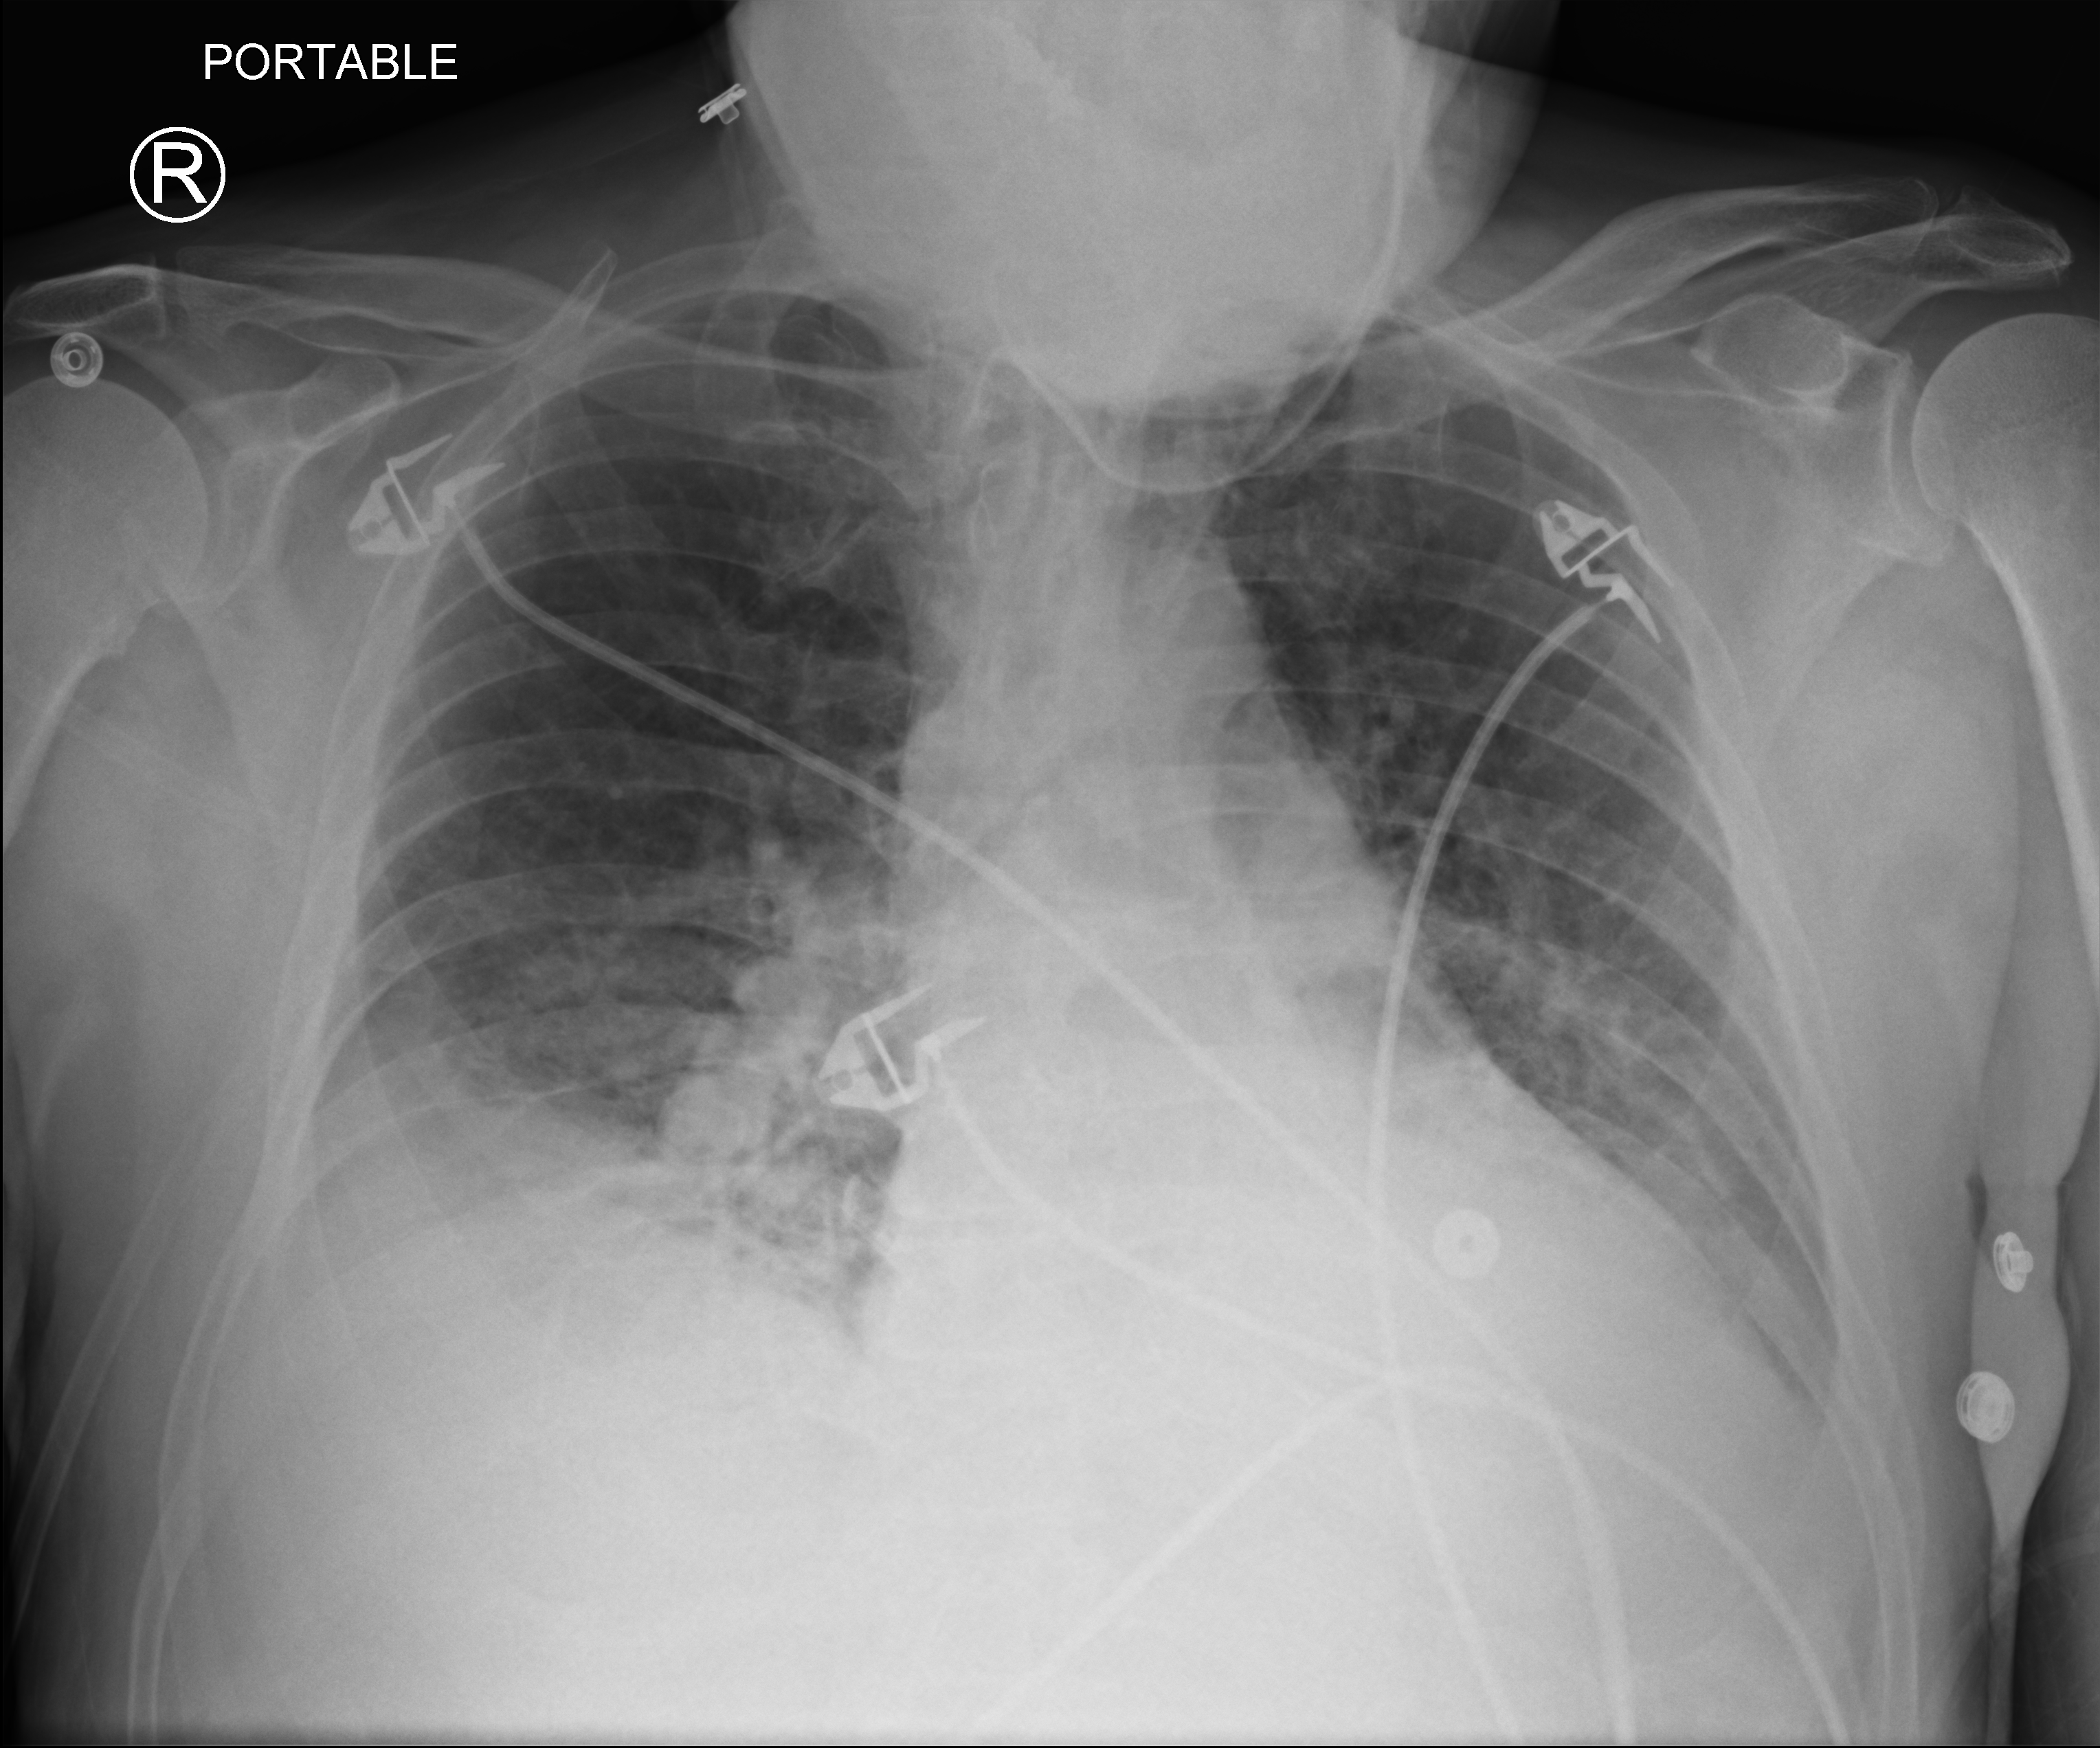
Portable chest radiograph, anteroposterior (AP) projection. Male patient hospitalised with COVID-19, age 18–59 years.
From the hospital-stay record, not from the radiograph (when in the stay this image was taken is not recorded): mechanically ventilated during this hospital stay: no; length of hospital stay: 16 days.